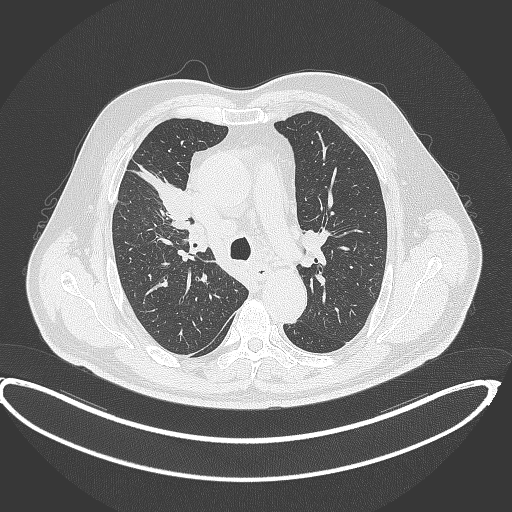
Chest CT, one axial slice. Position 277 of 390 along the scan axis. Reconstruction kernel B70f. 120 kVp. Lung window (W 1500 / L -600 HU). 1 mm slice thickness. 512 × 512 image matrix, field of view 448 × 448 mm. Patient: male, 62 years. Case-level facts recorded for this patient, not image findings: clinical TNM (as recorded): T1c N3 M1c.
Outlined on this slice (rectangle marked by the reading radiologist):
- lung tumour (recorded histology: adenocarcinoma): box from (x=135, y=165) to (x=195, y=219) px